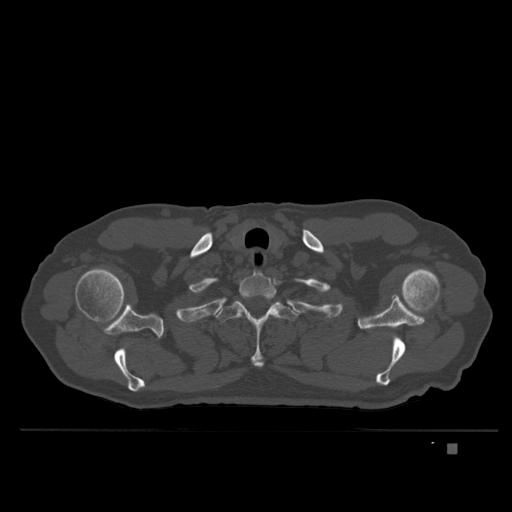
CT including the spine, one axial slice; position 317 of 435 along the scan axis; bone window (W 1800 / L 400 HU); 512 × 512 image matrix. Patient: male, 73 years. Case-level facts recorded for this patient, not image findings: primary cancer: skin.
Structures marked on this image (semi-automatic segmentation, software-assisted and operator-edited):
- T1 vertebra: bounding box (x1, y1, x2, y2) in pixels: (239, 271, 277, 314)
- T2 vertebra: (216, 294, 297, 367)